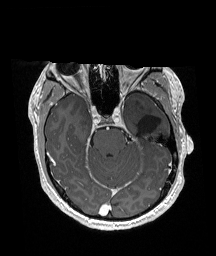
Brain MRI from a brain-tumour surgery series, one axial slice; T1-weighted post-contrast; 1 mm slice thickness; 216 × 256 image matrix, field of view 211 × 250 mm. Case-level facts recorded for this patient, not image findings: histopathology: Glioneuronal tumor; WHO grade: 2; tumour location: Left Superior Temporal Gyrus.
Outlined on this slice (manually delineated by an expert):
- previous resection cavity: bounding box <137,114,160,138> (left, top, right, bottom; pixels)